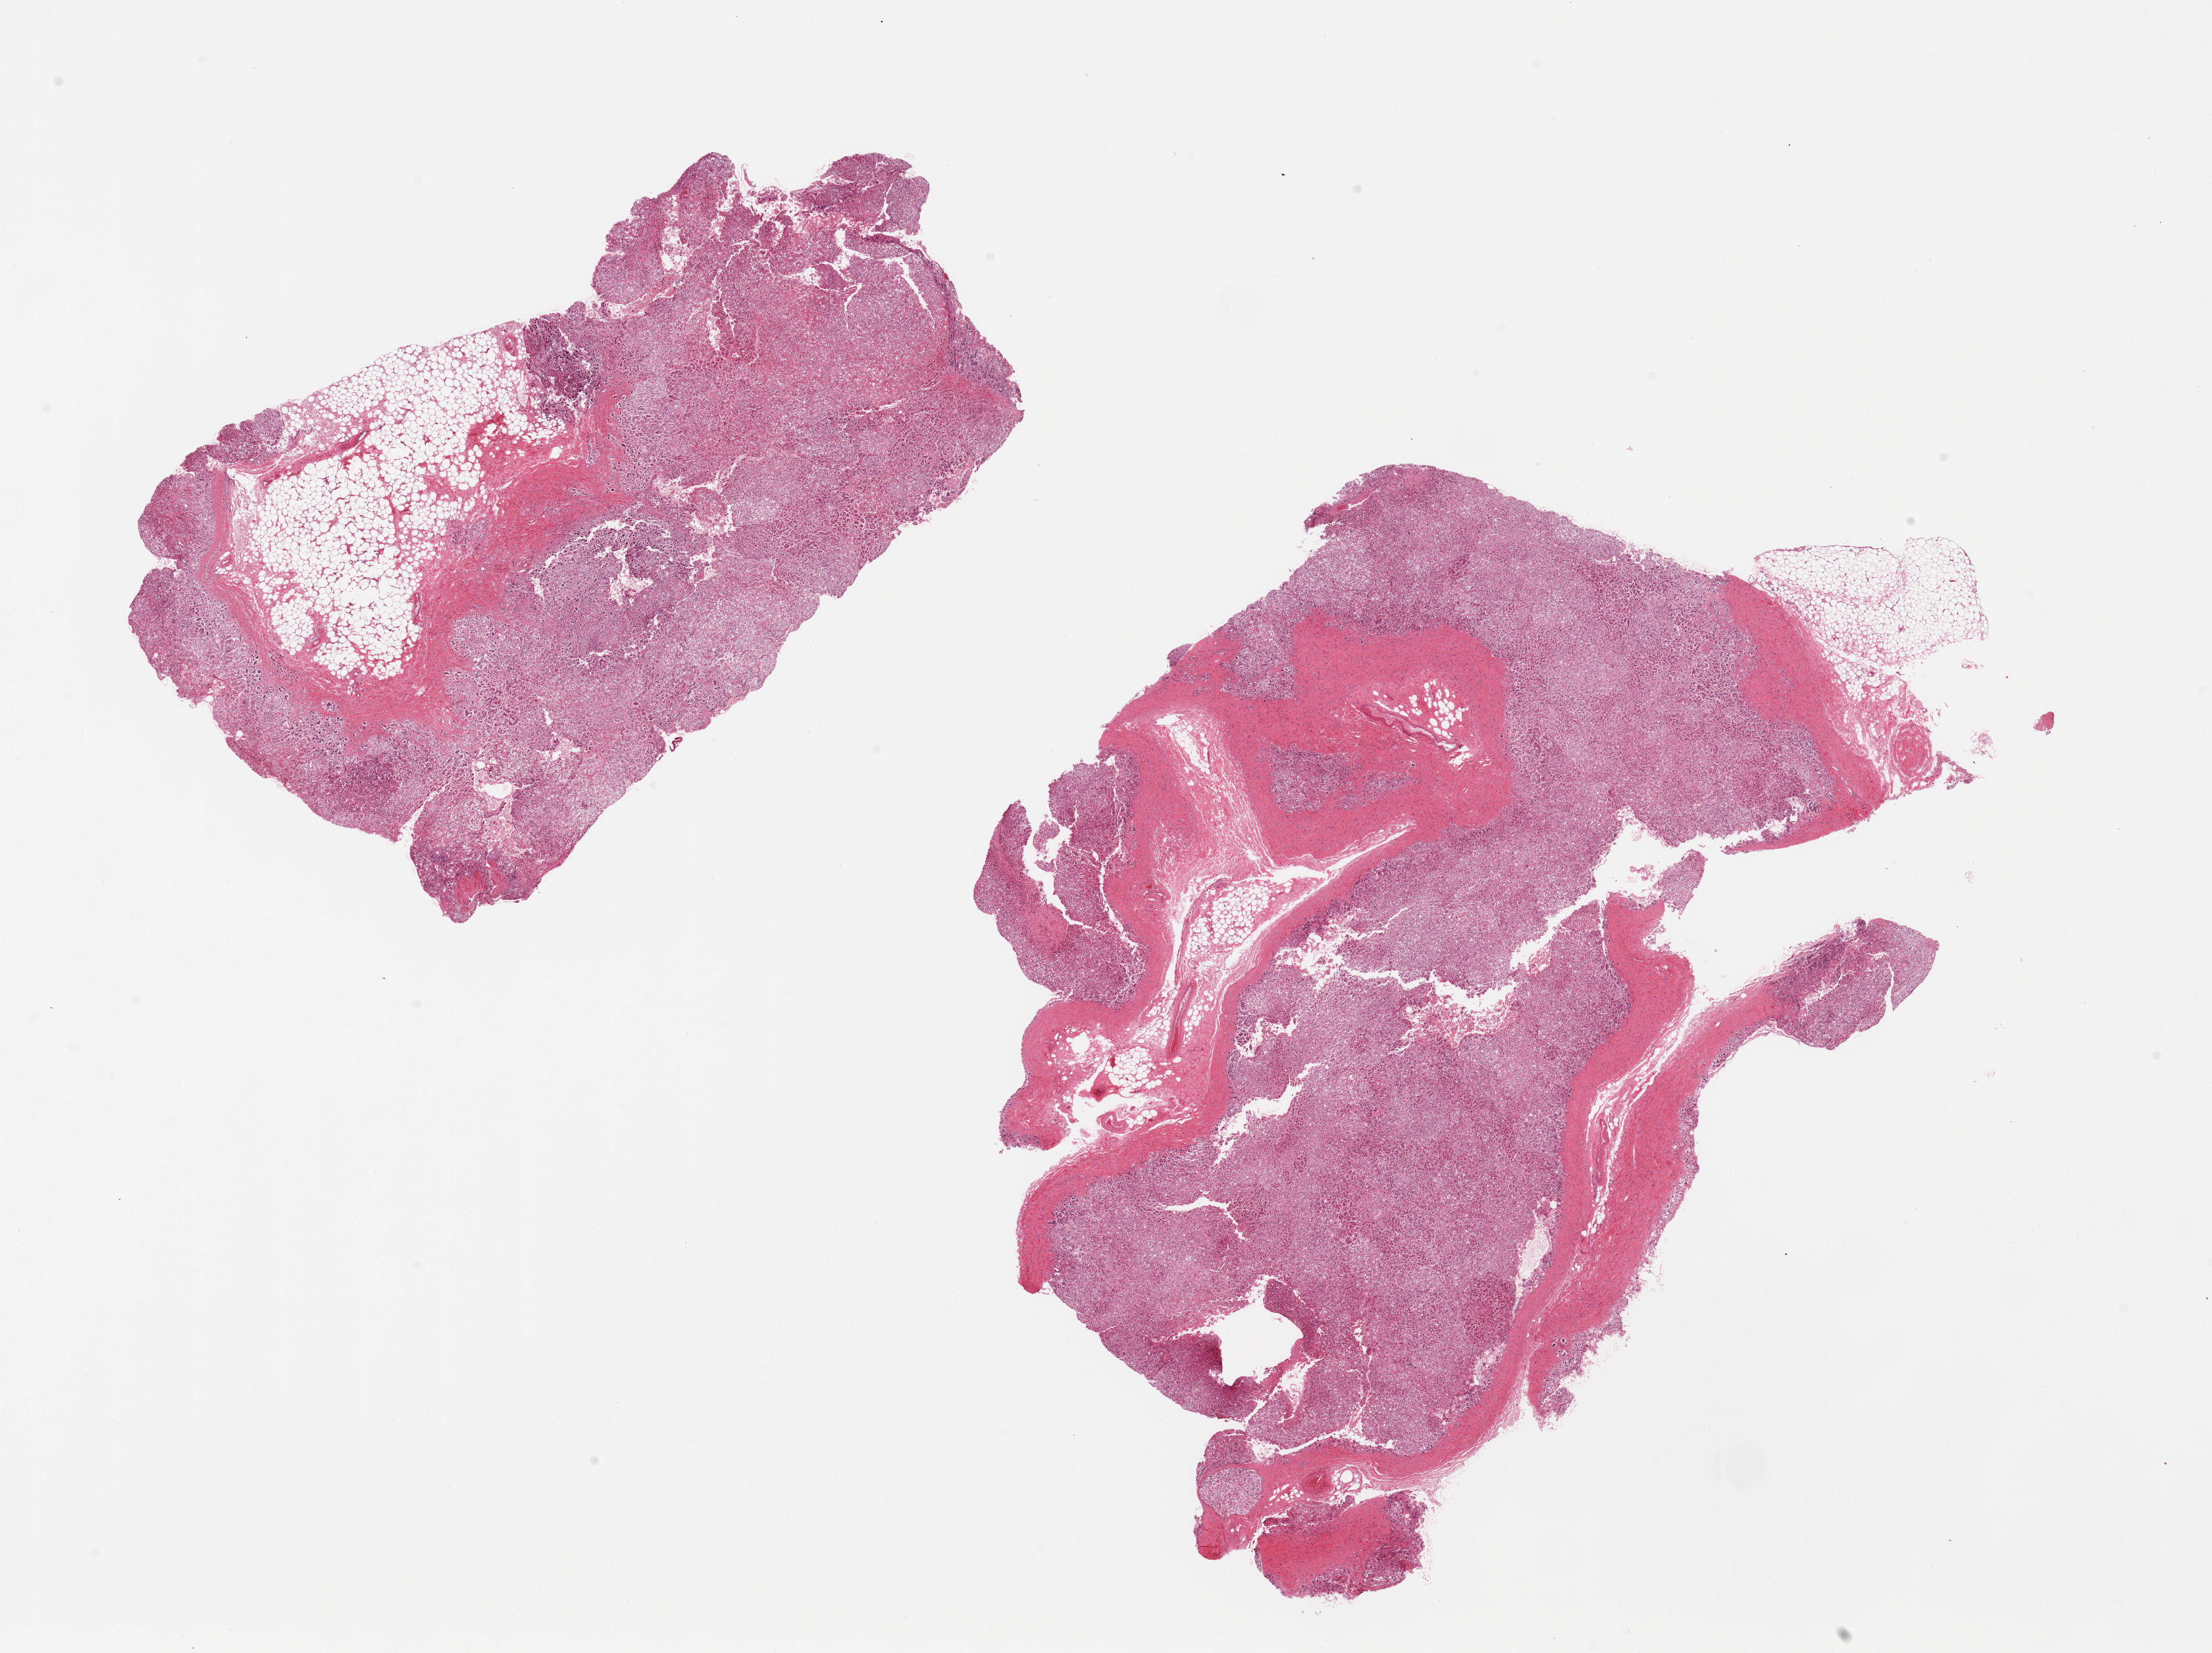
Whole-slide image, H&E stain, a low-resolution overview of the entire scanned area, about 26.6 x 19.9 mm (from a 20x scan); PAXgene-fixed, paraffin-embedded tissue; target tissue: adrenal gland; tissue donor sample.
- reviewer comment on this tissue sample: 2 pieces, all cortex, ~30% adherent fat/fibrous tissue